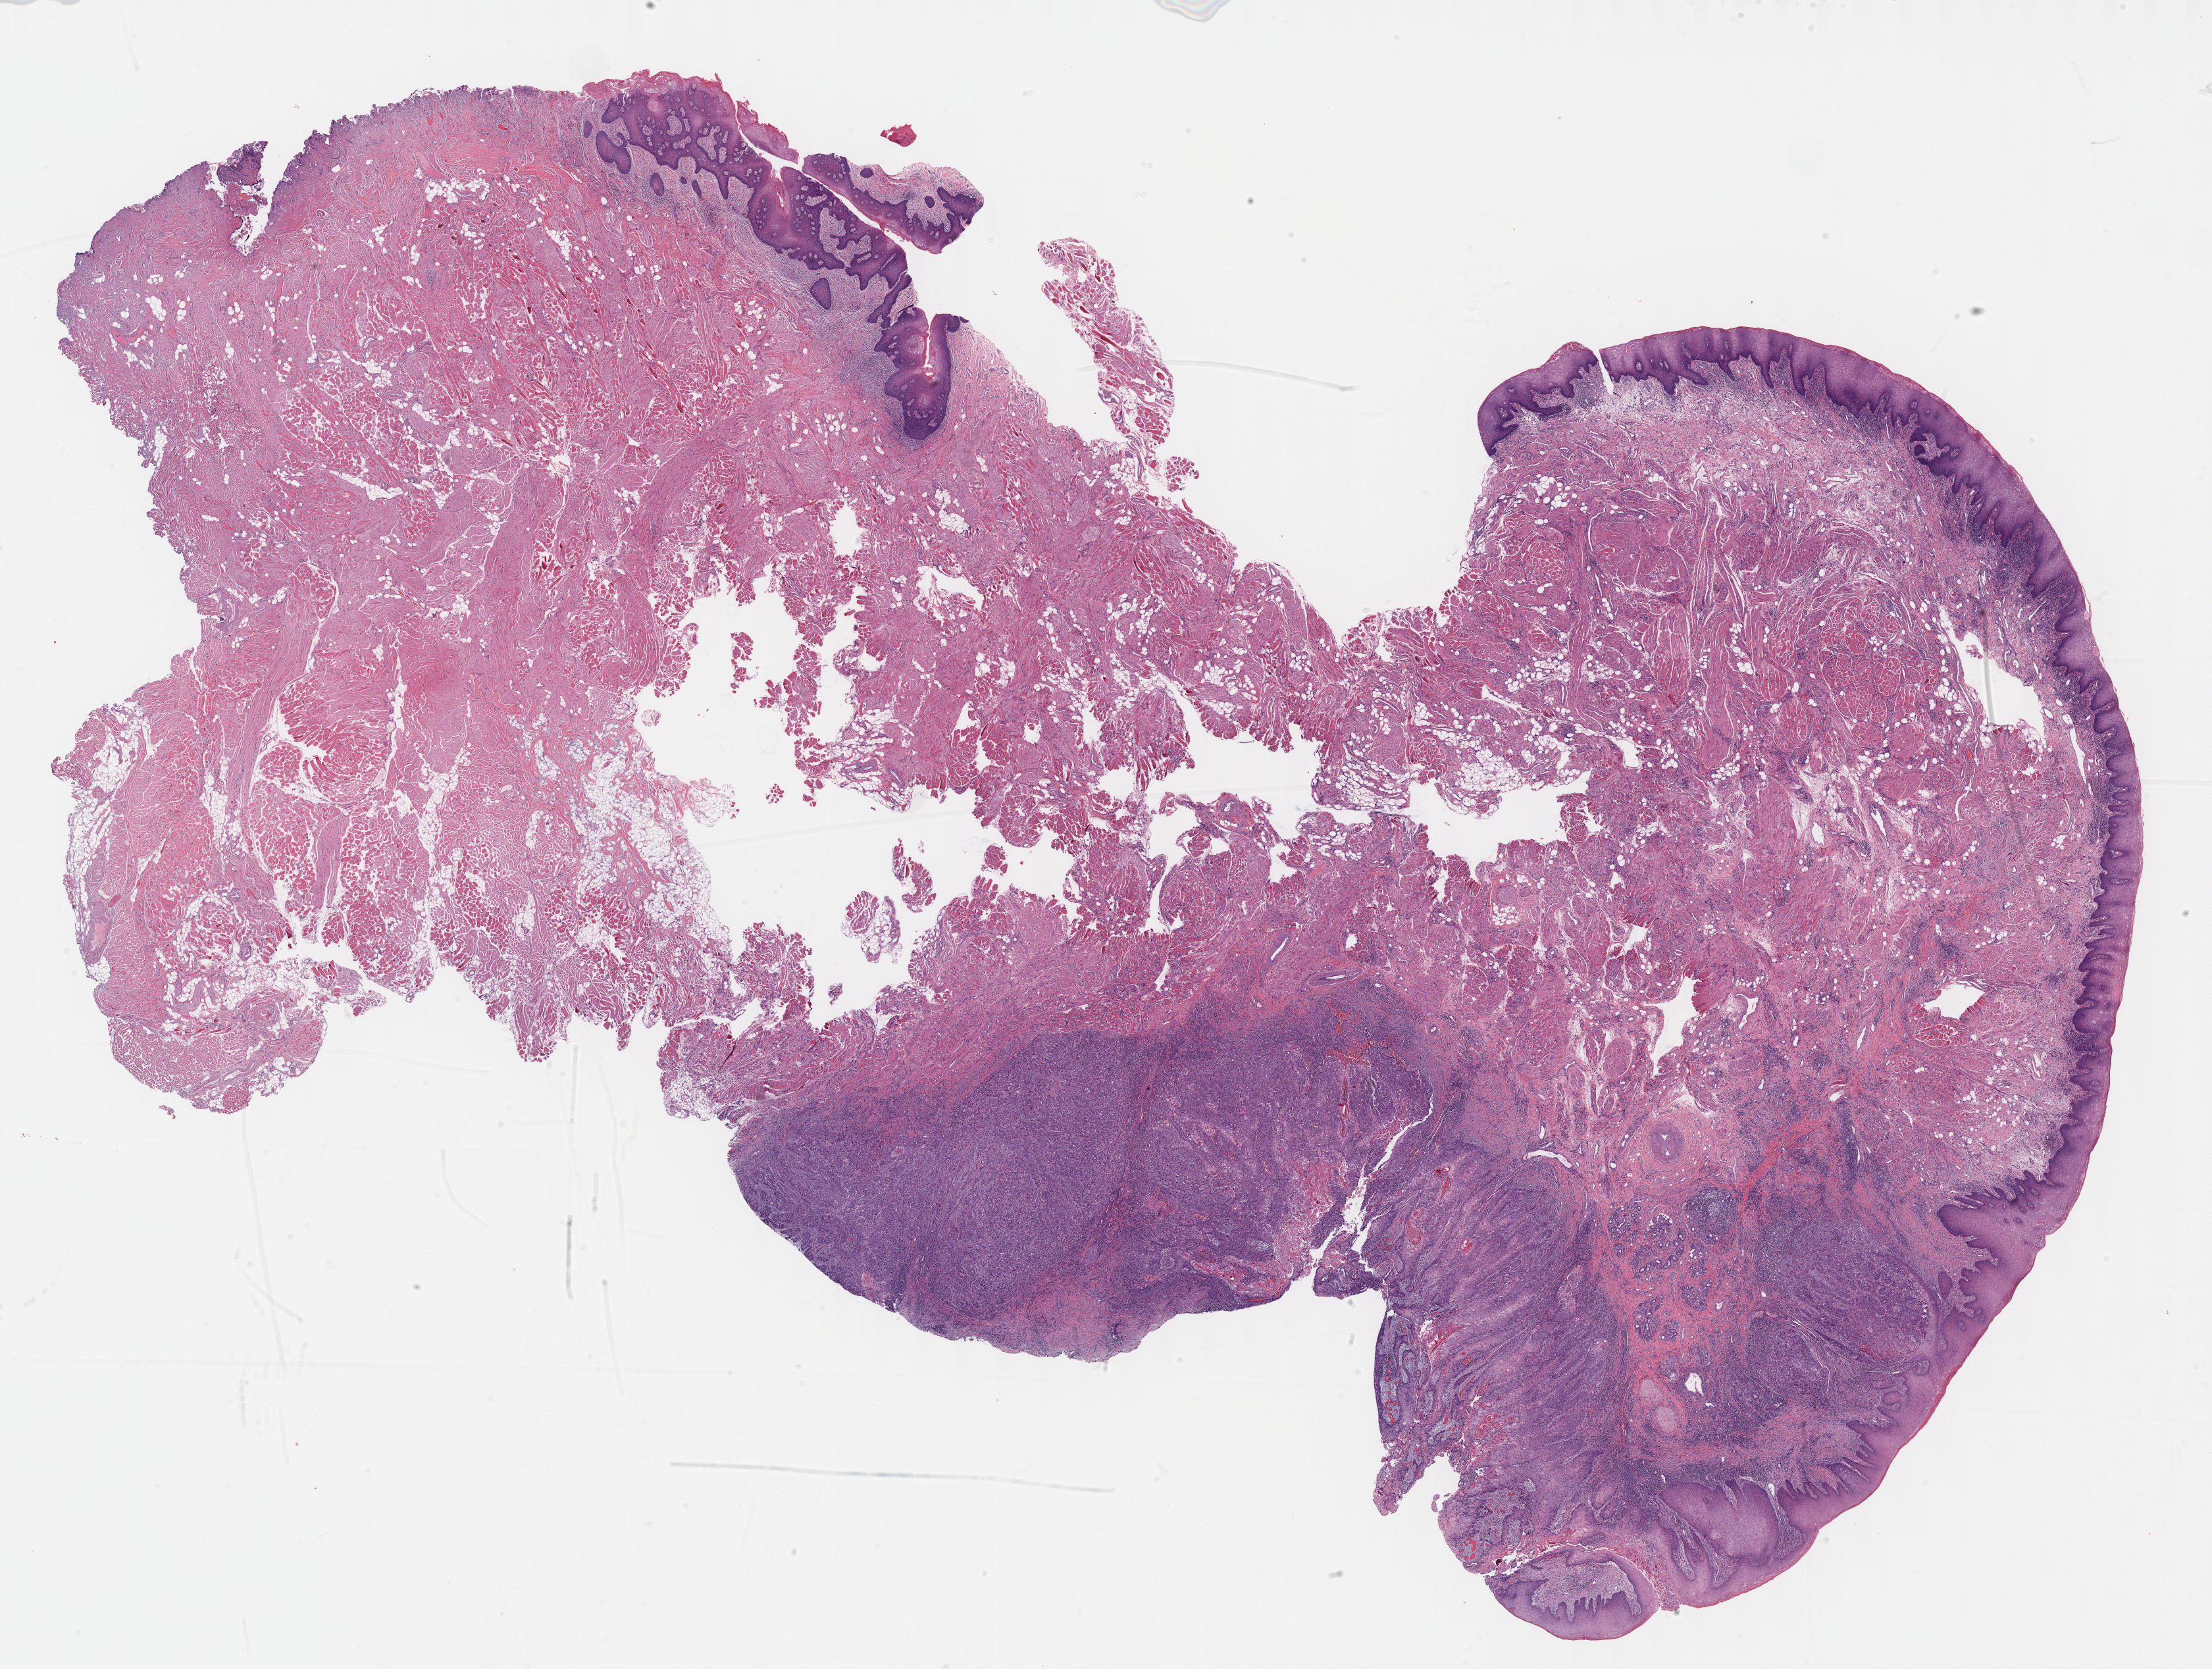
Whole-slide histology image, H&E-stained, low-resolution overview of the scanned area, about 27.2 x 20.5 mm, formalin-fixed paraffin-embedded (FFPE) diagnostic section, head and neck, primary tumour sample. Patient: male, age at initial diagnosis 68 years. Histologic grade: G2 (moderately differentiated).
• AJCC pathologic stage: II (7th edition)
• TNM: T2 N0 M0
• diagnosis: Squamous cell carcinoma, NOS (mouth, NOS)